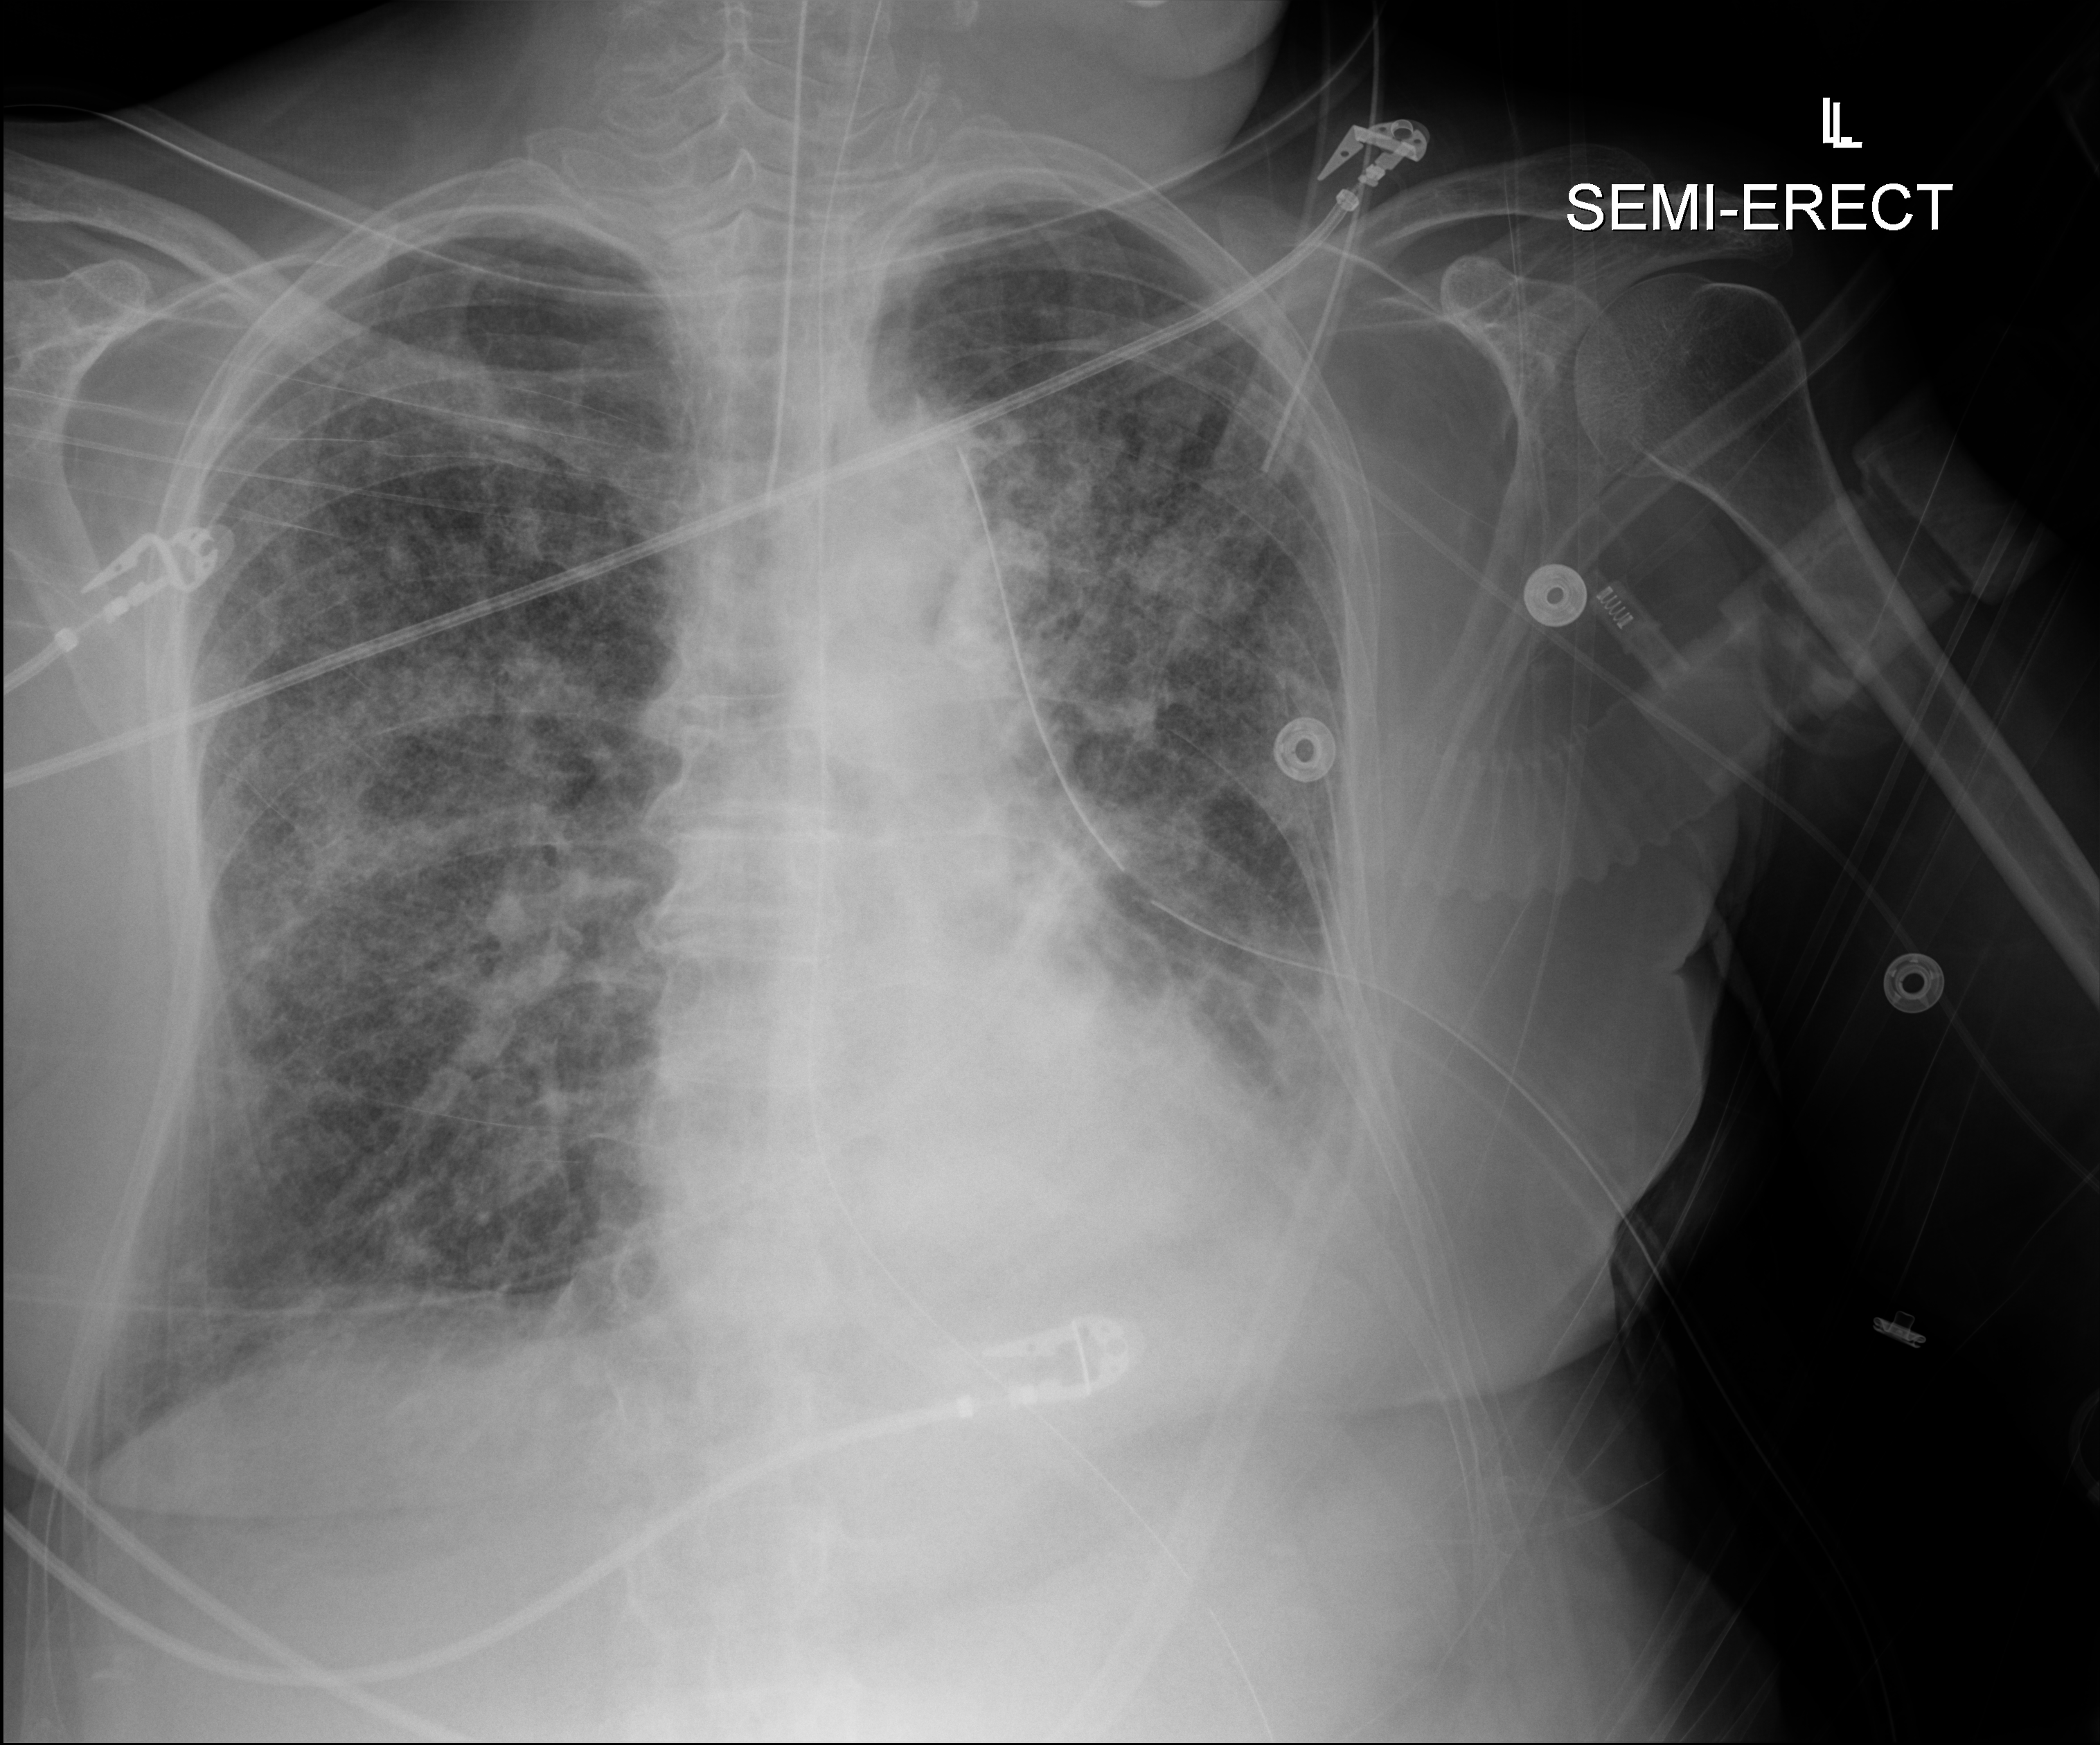
Chest X-ray (portable). Patient hospitalised with COVID-19; female, aged 75–90 years.
Hospital-stay facts (about this admission, not read from this image; timing relative to this image not recorded): mechanically ventilated during this hospital stay: yes.